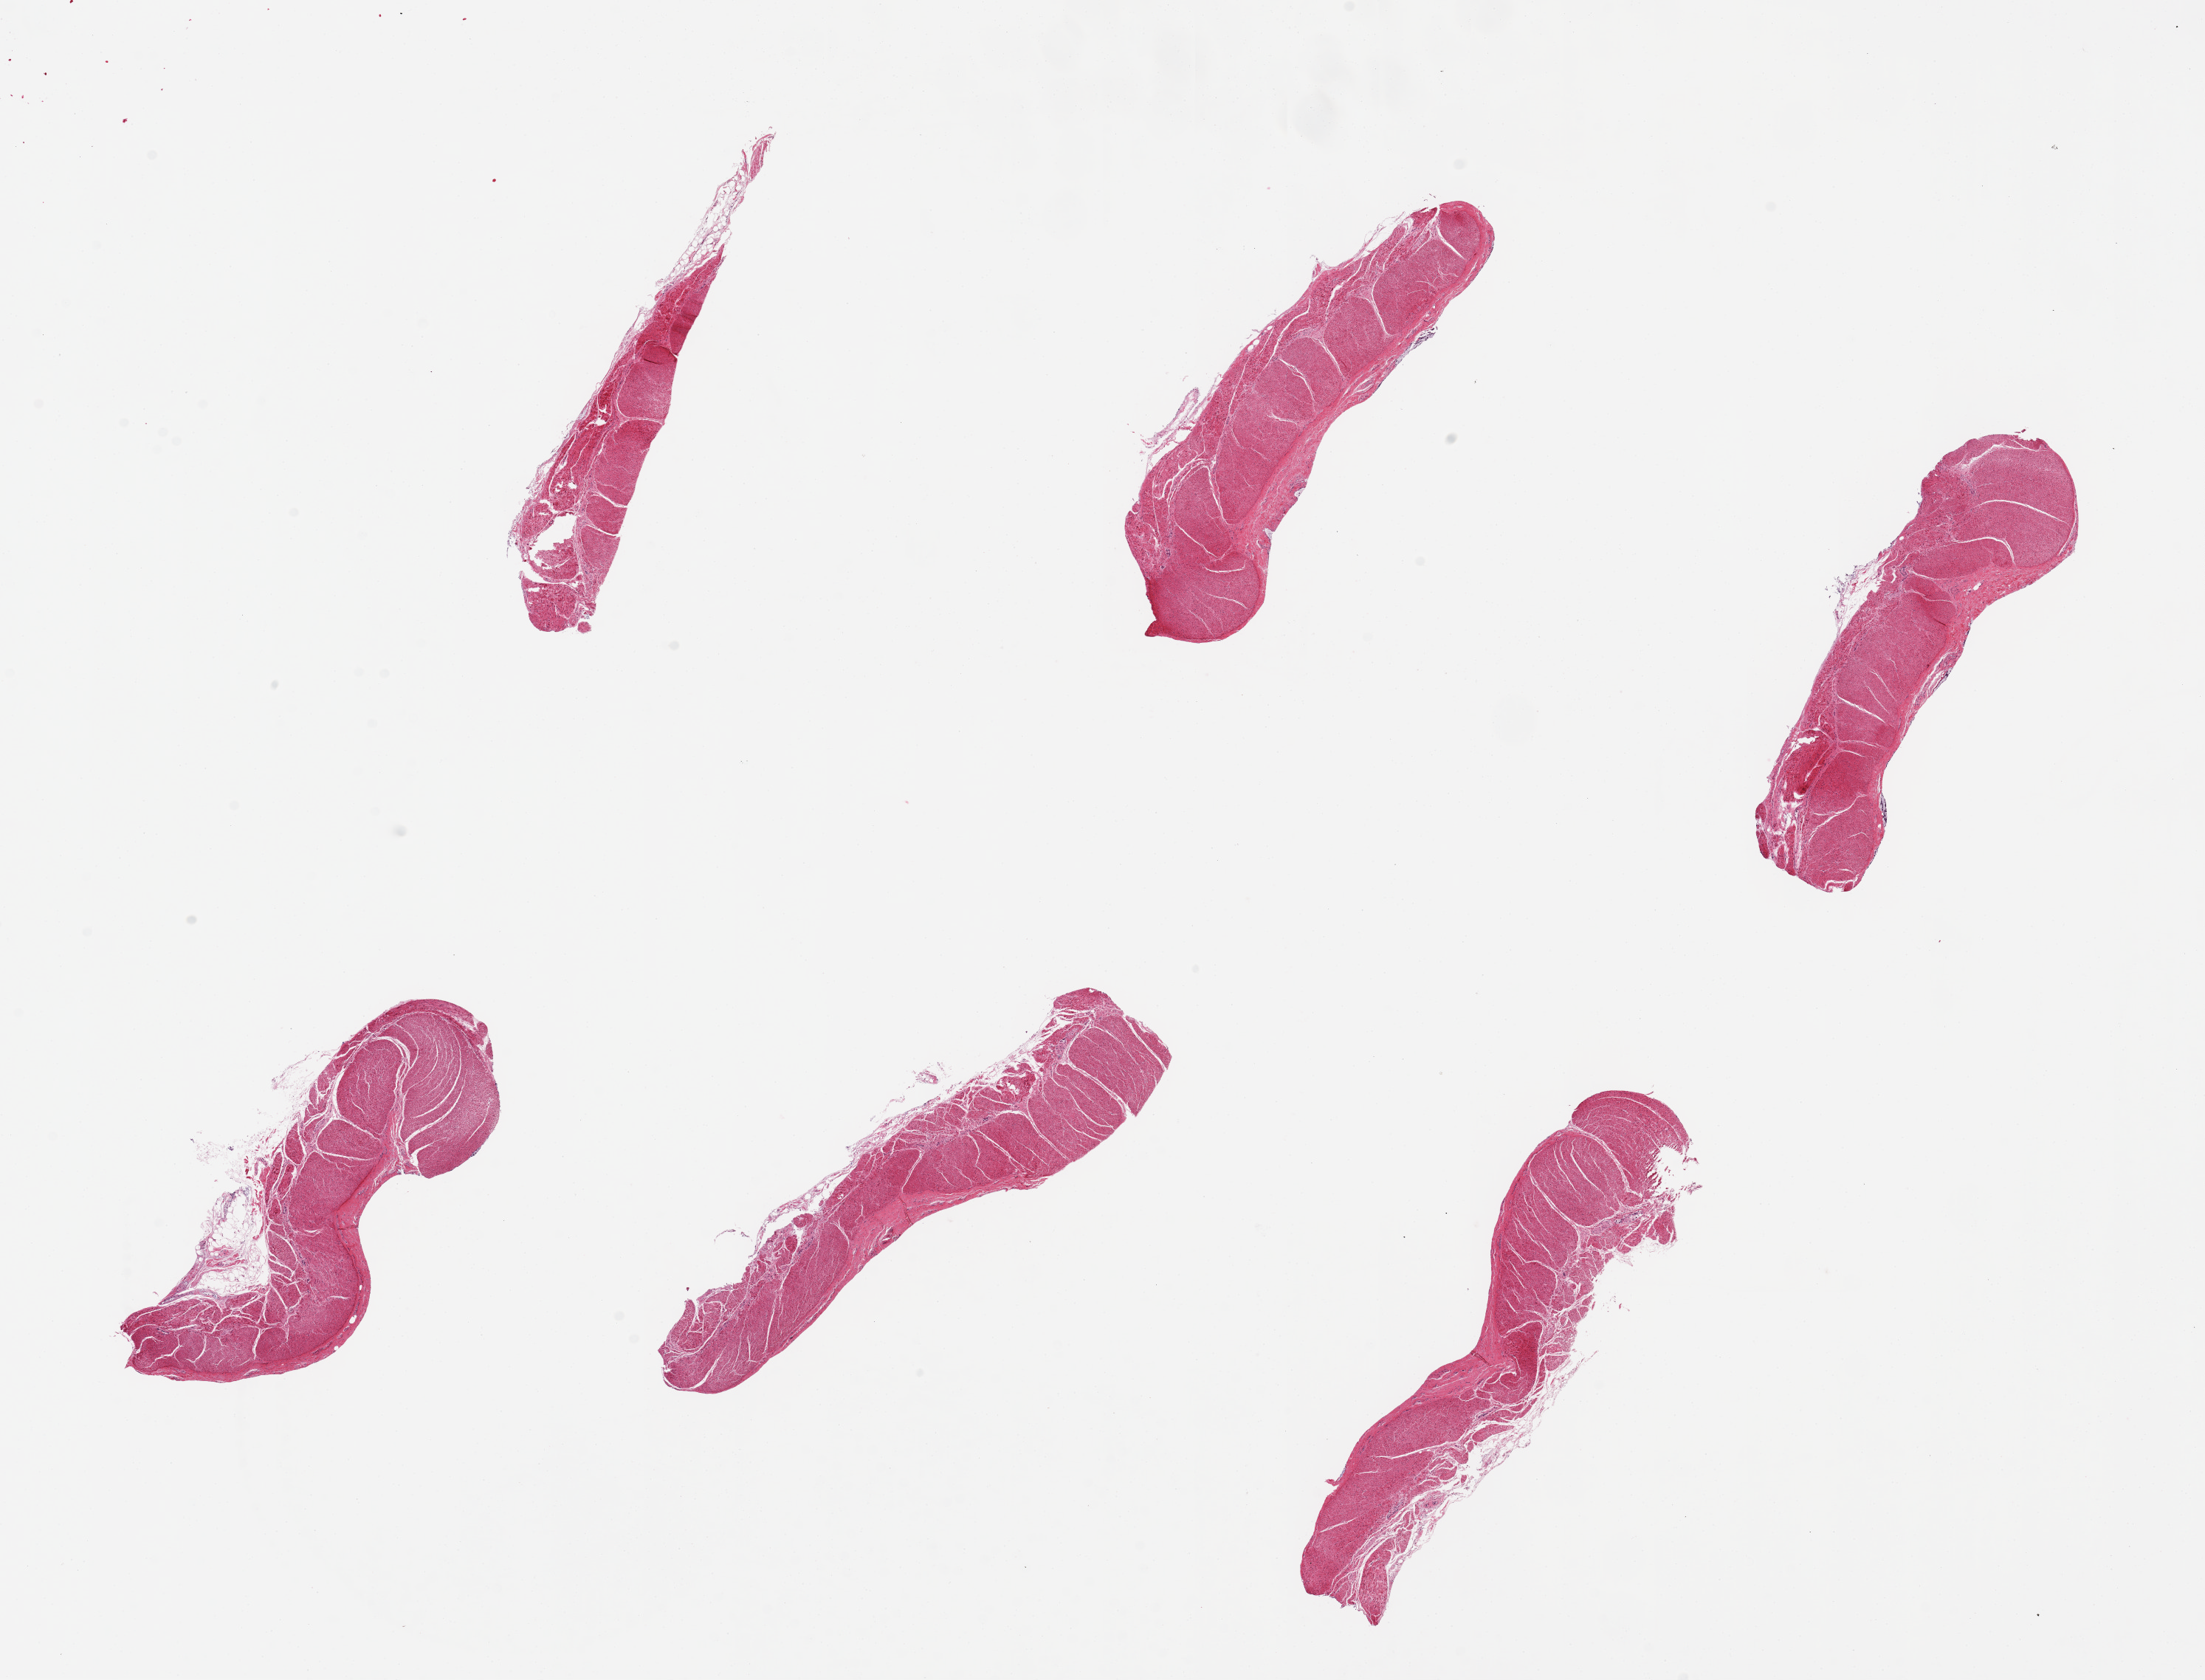
Hematoxylin and eosin (H&E) whole-slide image — whole scanned area (about 23.6 x 18.0 mm) shown as a low-resolution overview. PAXgene-fixed, paraffin-embedded tissue. Sampled site (target tissue): sigmoid colon. Tissue donor sample. Donor: female.
Reviewer comment on this tissue sample: 6 pieces, up to 6x2mm; well dissected muscle.